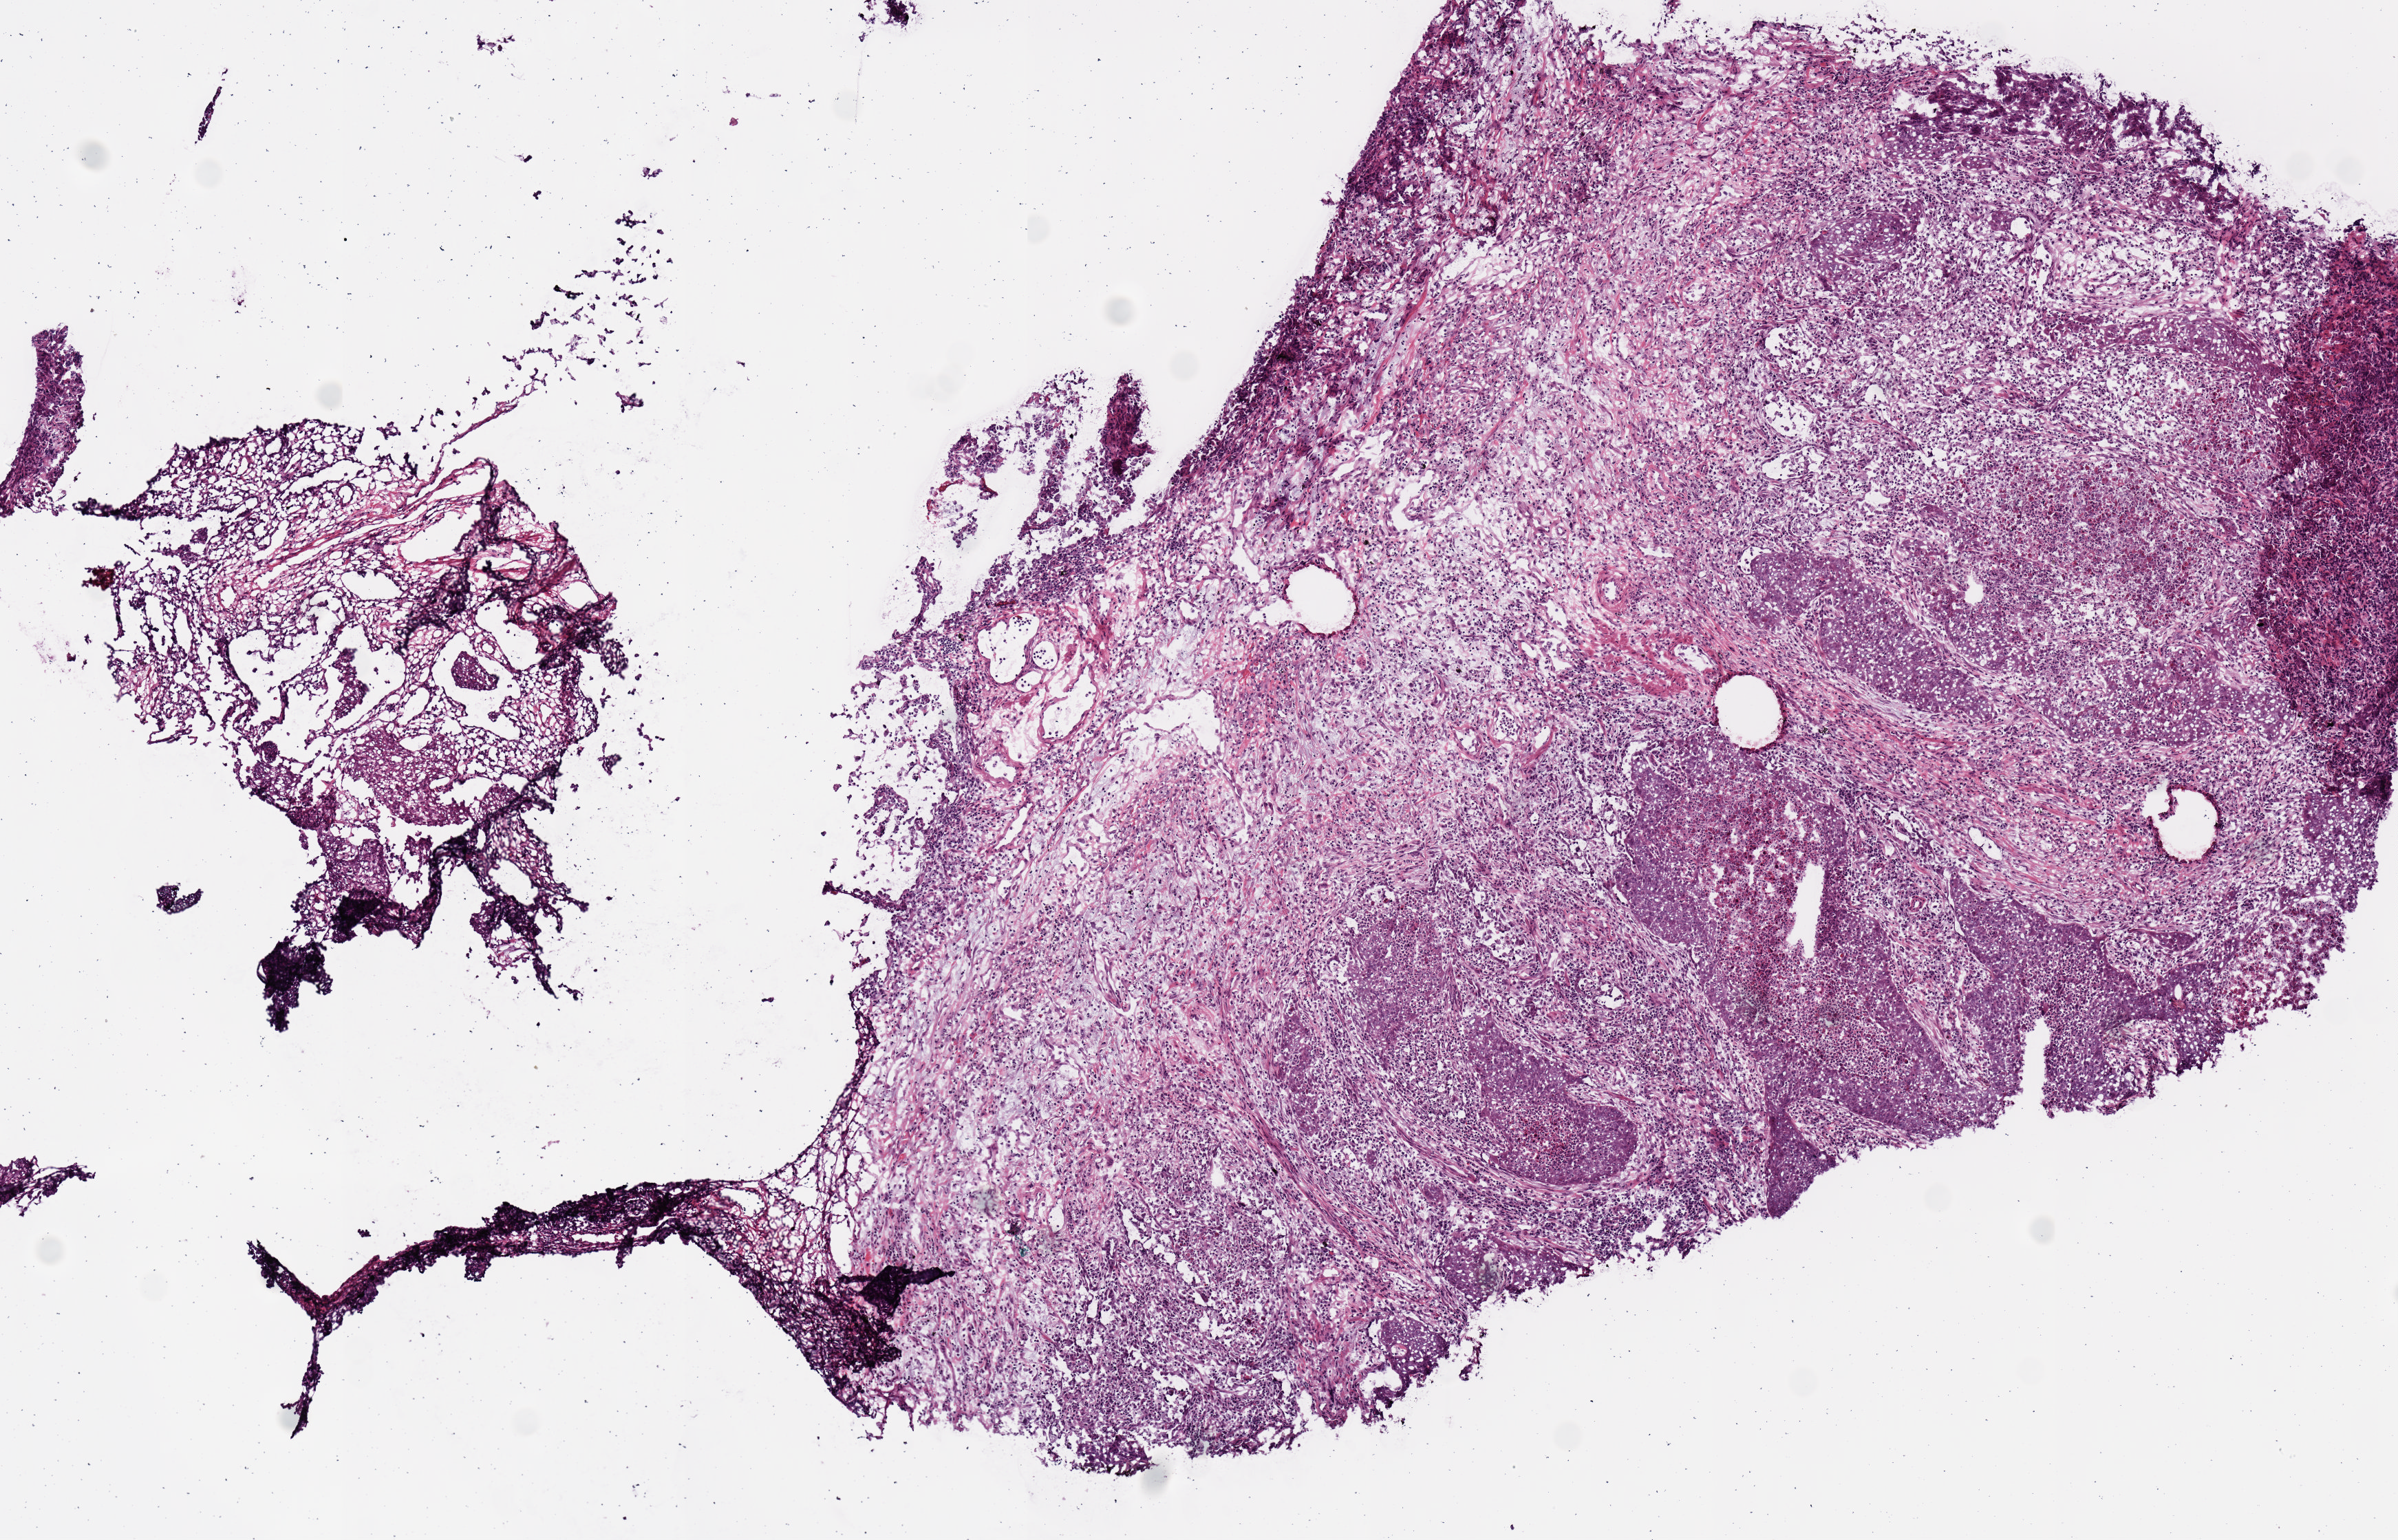
H&E whole-slide image — low-resolution overview of the scanned area, about 6.9 x 4.4 mm, frozen section from the bottom of the tissue portion, lung, primary tumour sample. Female patient; age at initial diagnosis 66 years.
- pathologic diagnosis: Squamous cell carcinoma, NOS (lower lobe, lung)
- AJCC pathologic stage: IIB (6th edition)